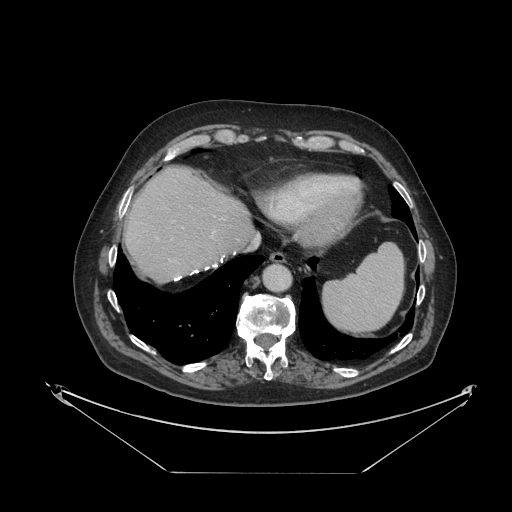
Contrast-enhanced abdominal CT, one axial slice; position 102 of 121 along the scan axis; reconstruction kernel STANDARD; intravenous contrast given; soft-tissue window (W 400 / L 40 HU); 2.5 mm slice thickness; 512 × 512 image matrix, field of view 500 × 500 mm. Male patient, age 68 years. Case-level facts recorded for this patient, not image findings: diagnosis: colorectal cancer liver metastases, imaged before liver resection; multiple liver metastases: no; largest metastasis: 4 cm; disease in both lobes: no.
Outlined on this slice (expert manual segmentation):
- liver: bounding box [x1, y1, x2, y2] px = [126, 168, 253, 281]
- planned liver remnant (the part of the liver to remain after resection): [126, 168, 253, 282]